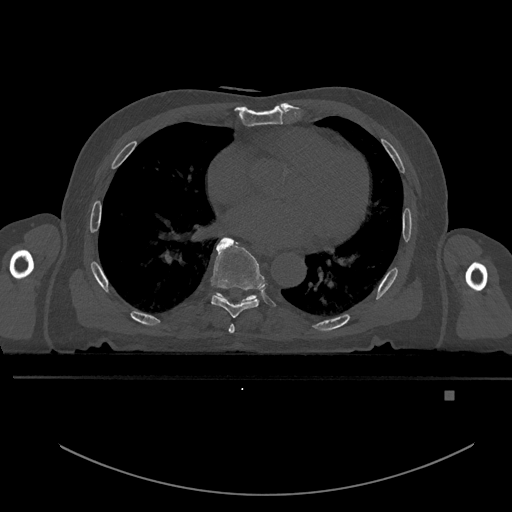
CT including the spine, one axial slice; slice 245 of 969 in the series (ordered by position); bone window (W 1800 / L 400 HU); 512 × 512 image matrix, field of view 456 × 456 mm. Male patient, age 82 years. From the clinical record (not read from this slice): primary cancer: prostate; vertebrae with lytic lesions (as recorded): T11, T9, T8, T2.
Structures marked on this image (semi-automatic segmentation, software-assisted and operator-edited):
- T6 vertebra: bounding box [x1, y1, x2, y2] px = [229, 324, 235, 333]
- T7 vertebra: [211, 237, 265, 318]
- T8 vertebra: [213, 293, 258, 304]